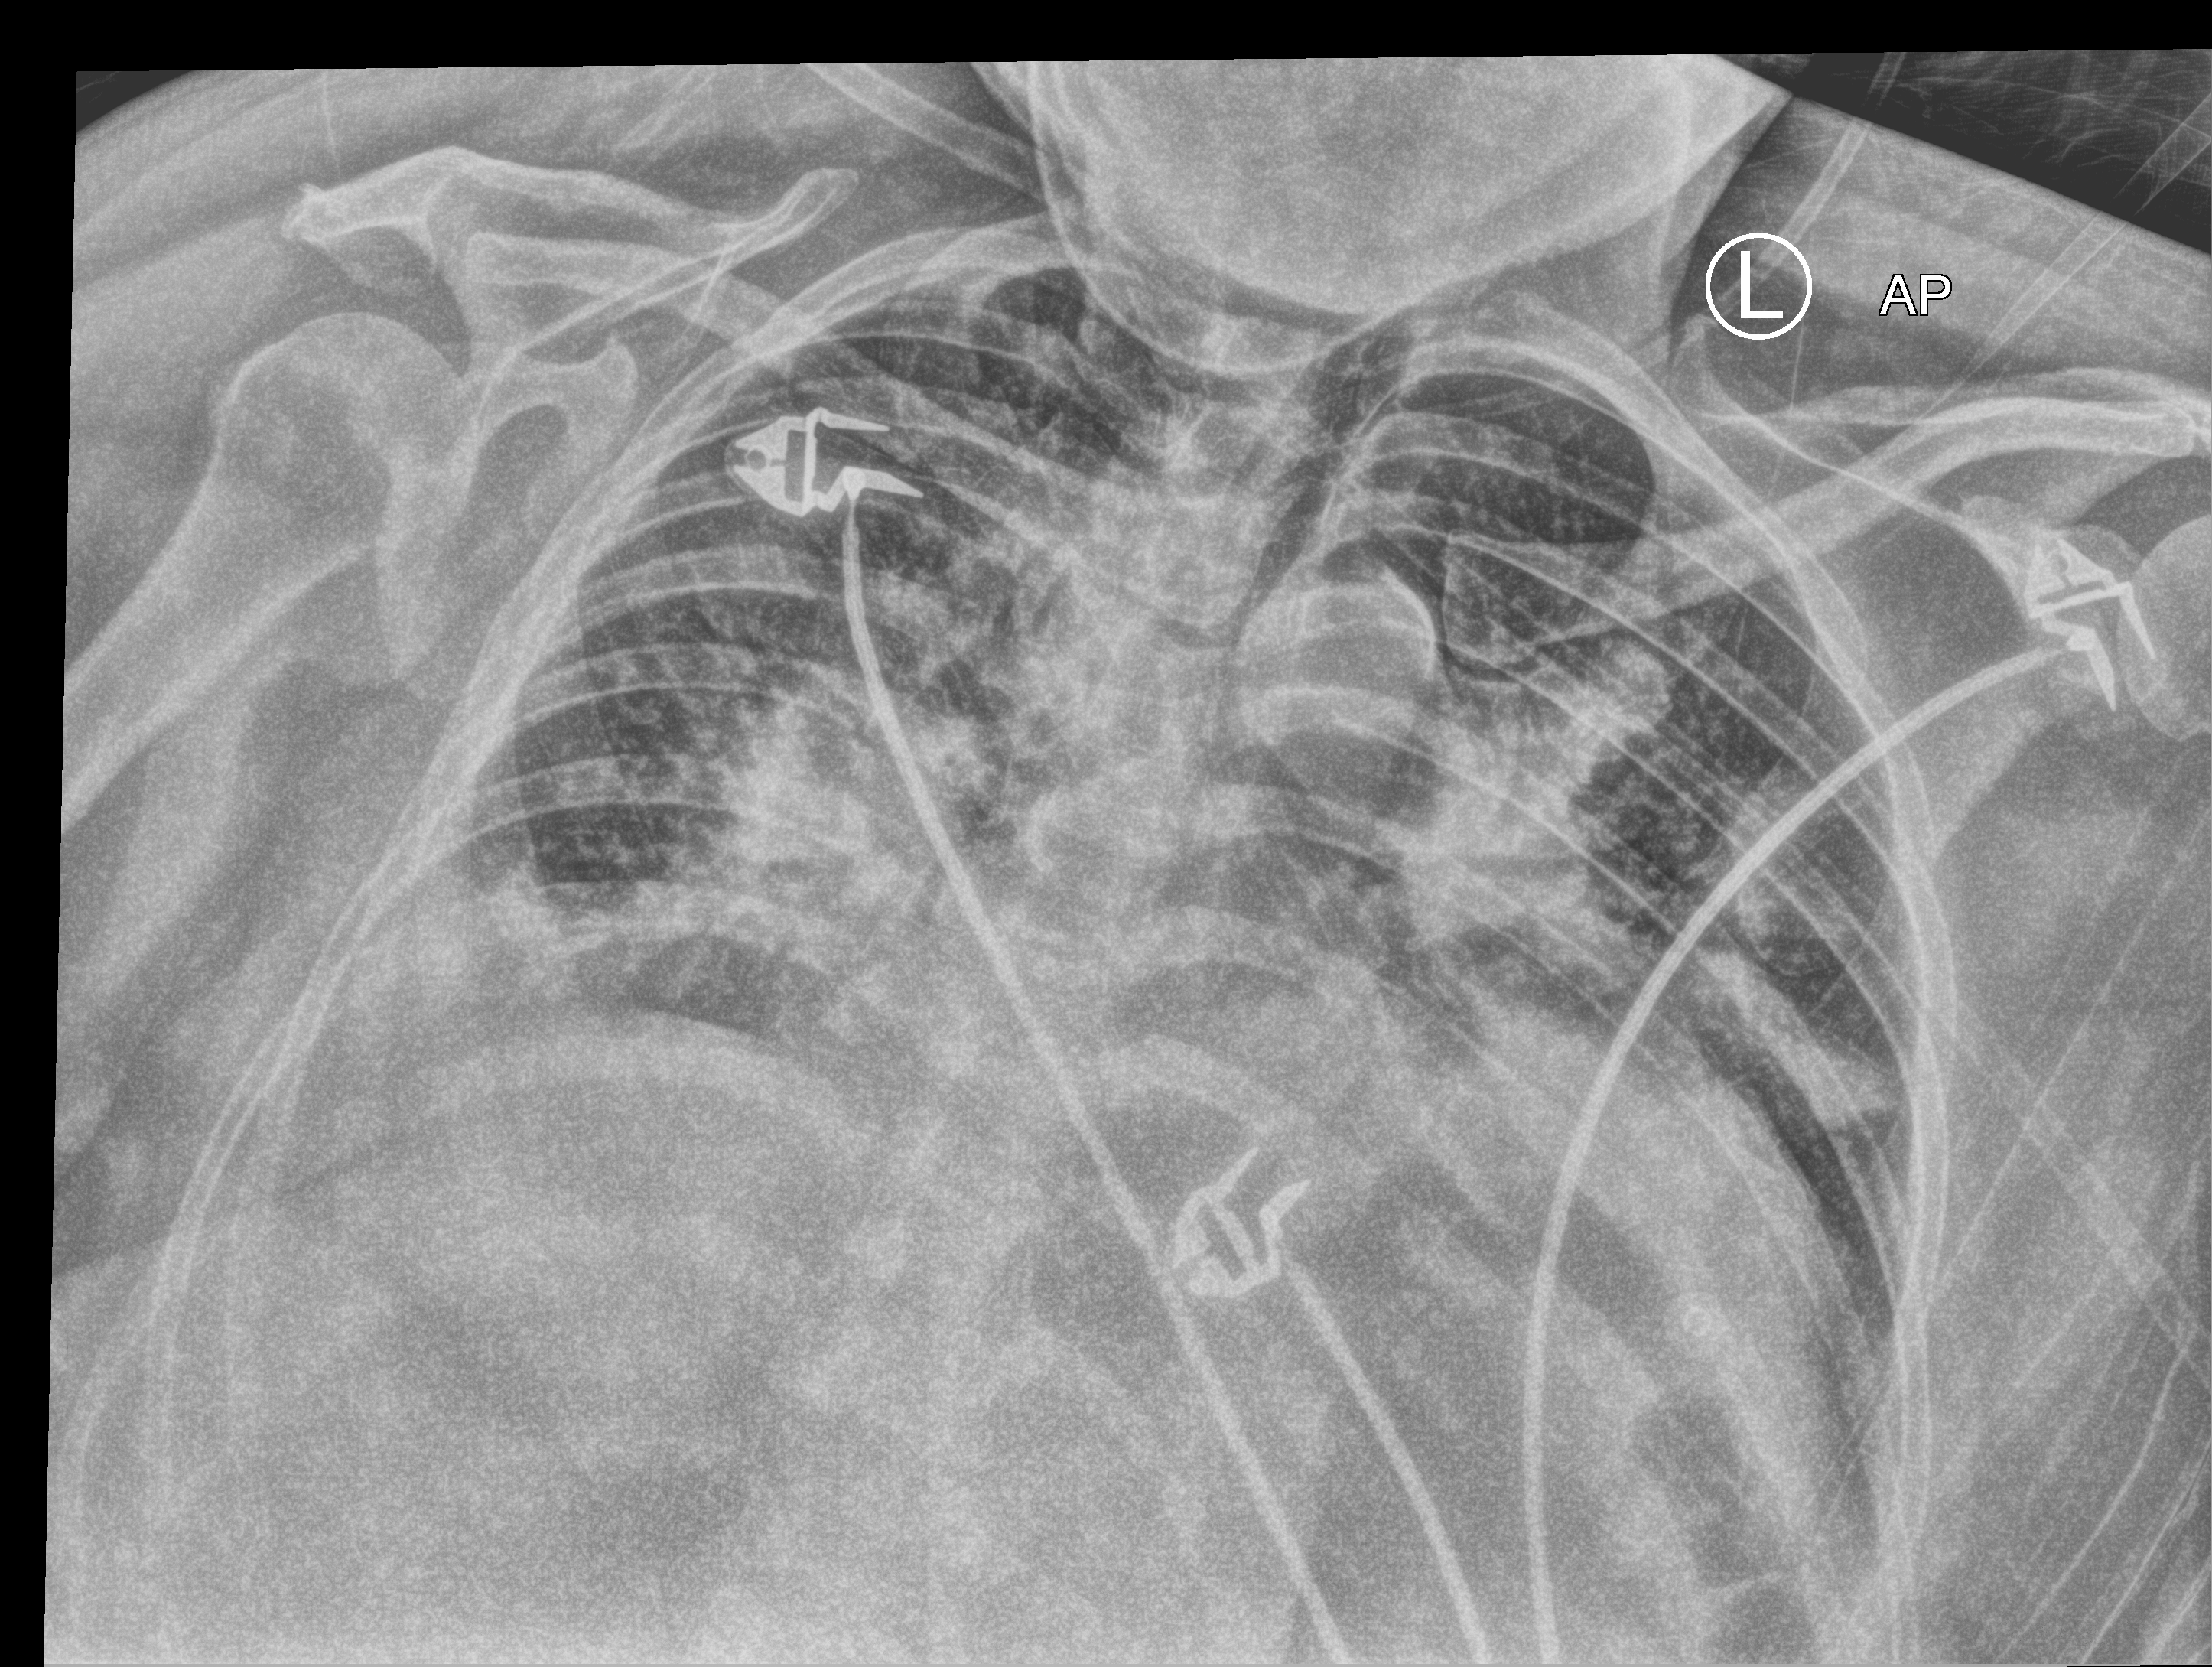
Chest X-ray (portable), anteroposterior (AP) projection. Female patient hospitalised with COVID-19, age 18–59 years.
Admission-level facts for this patient (not findings on this image; timing relative to this image not recorded):
- admitted to intensive care during this hospital stay: no